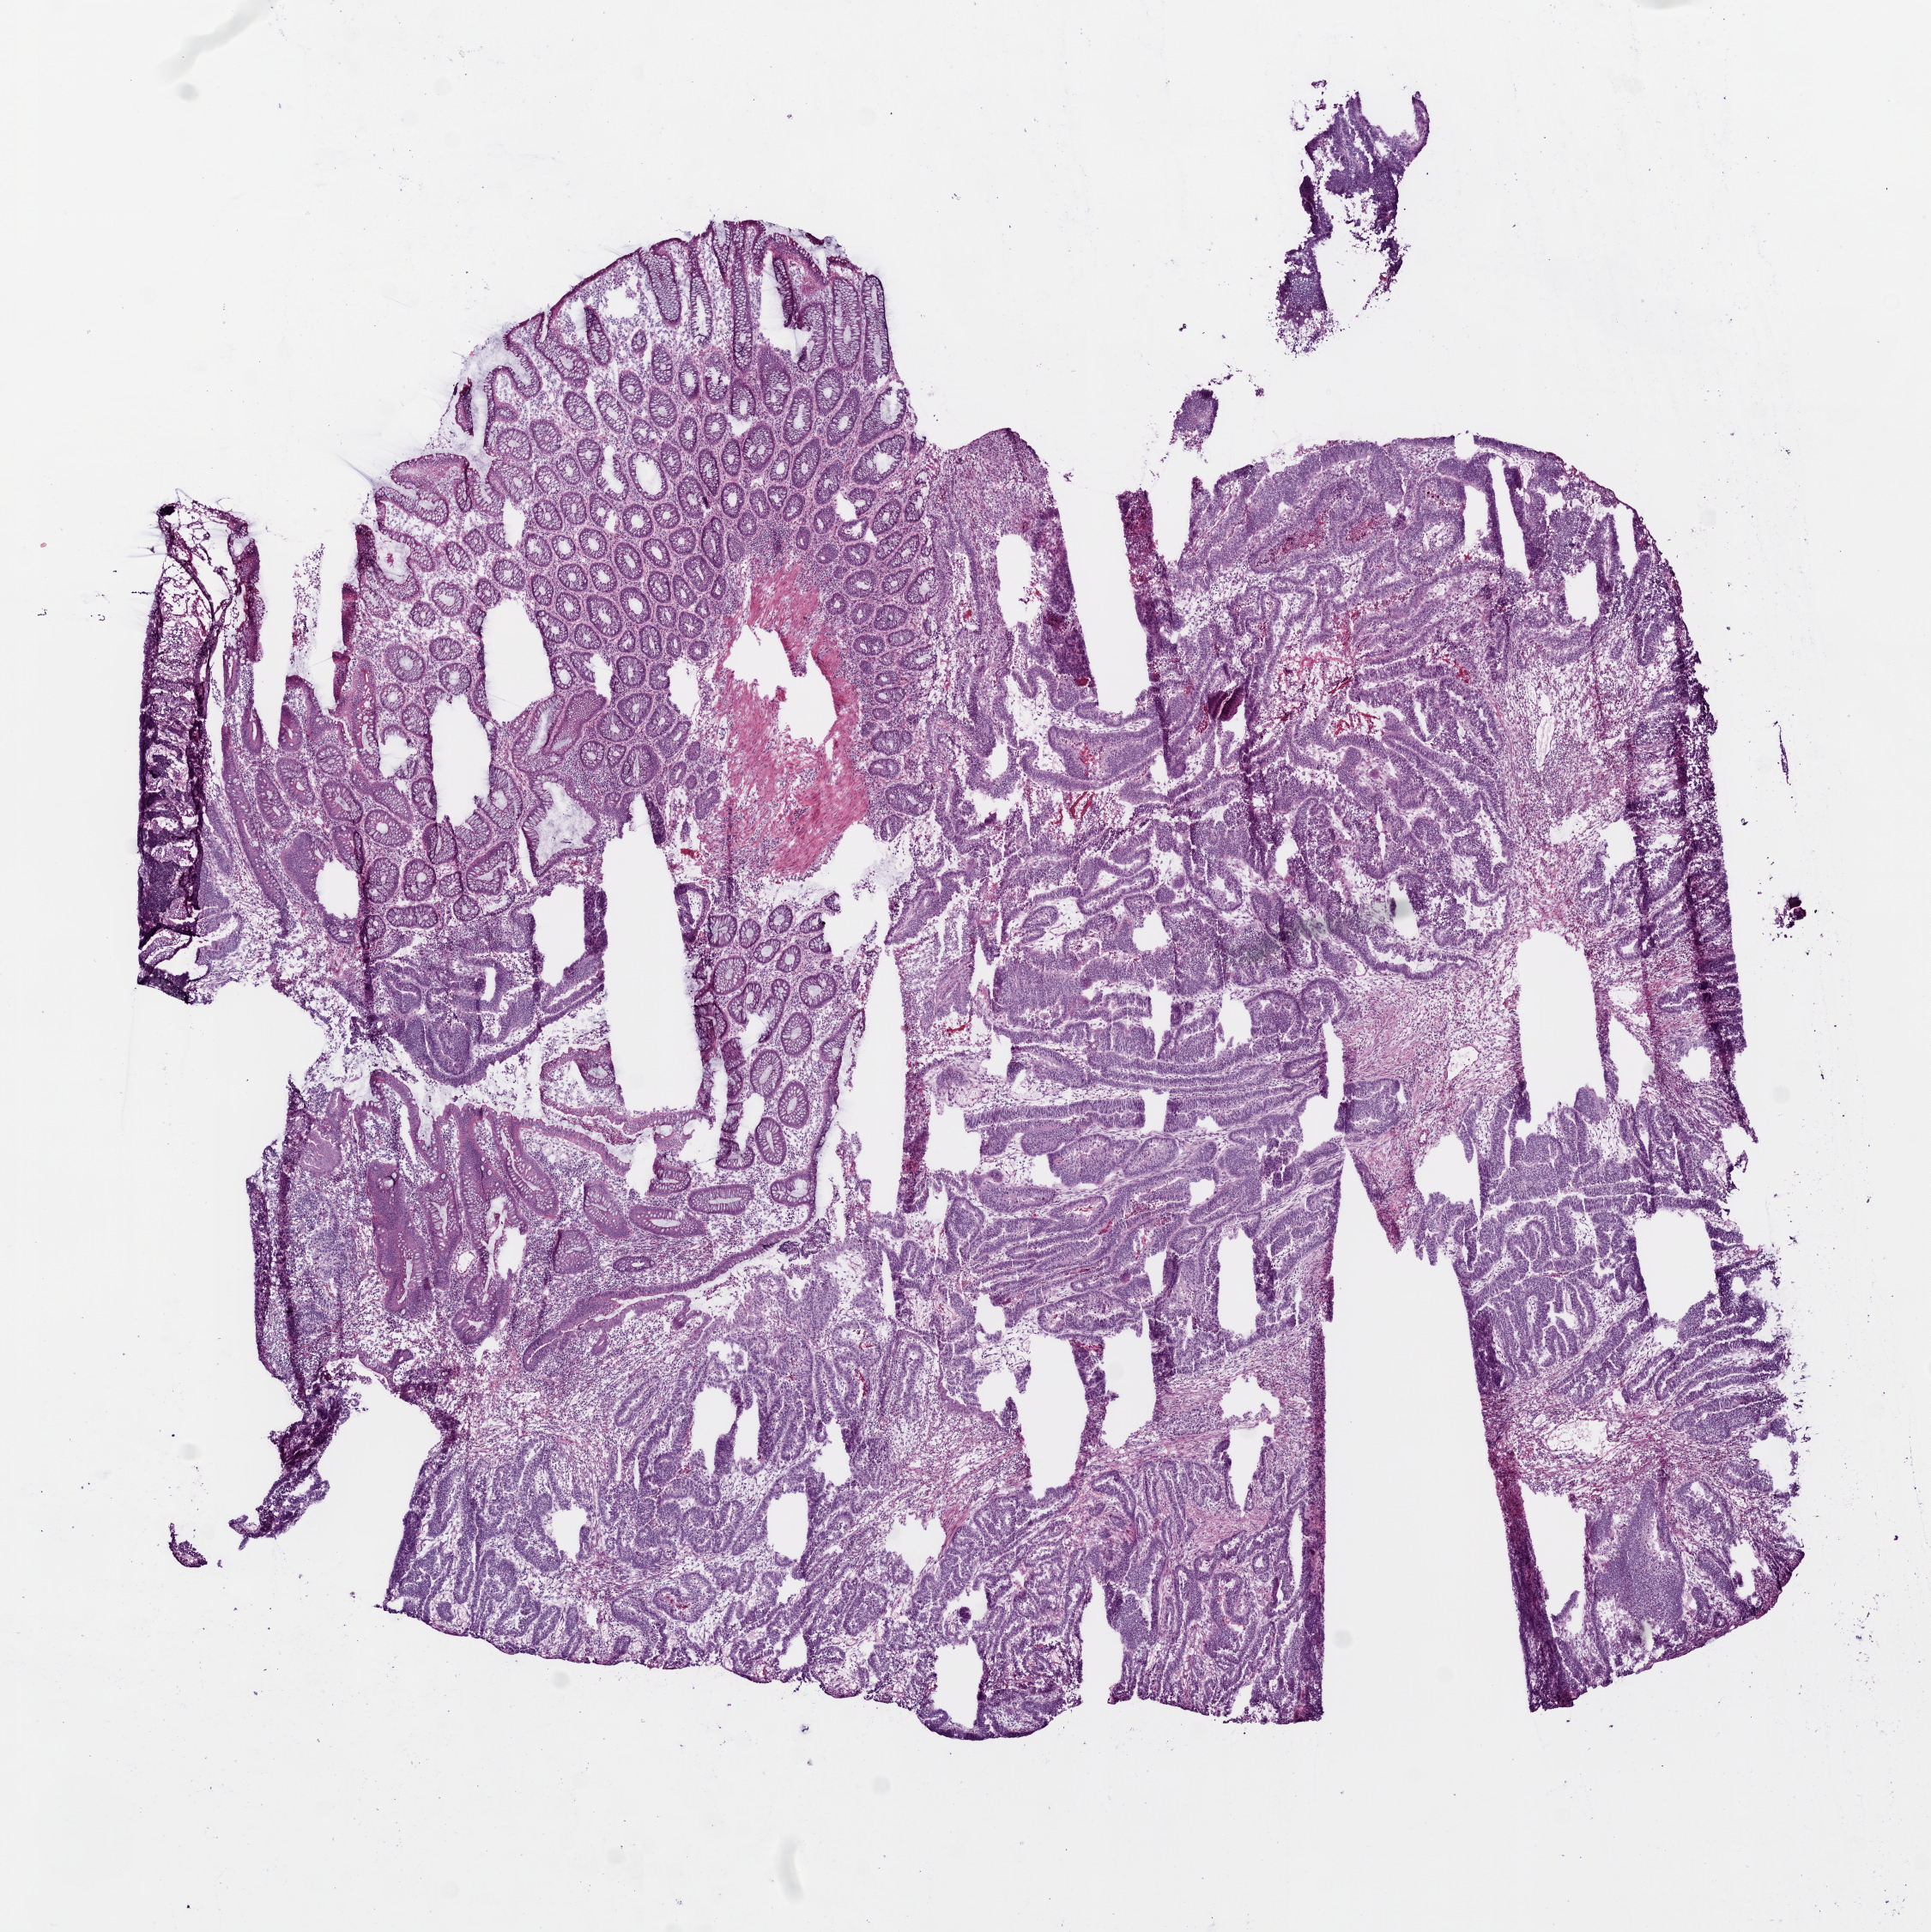
Hematoxylin and eosin (H&E) stained whole-slide image, whole scanned area (about 9.0 x 9.0 mm) shown as a low-resolution overview; frozen section from the bottom of the tissue portion; sample: primary tumour, rectum. Female, age 67 years at initial diagnosis. Composition of this section per pathologist review: tumour cells 59%, tumour nuclei 60%, normal cells 30%, stromal cells 8%, necrosis 3%.
• pathologic diagnosis: Adenocarcinoma, NOS (rectosigmoid junction)
• lymph nodes positive (case pathology): 0 of 26 examined
• AJCC pathologic stage: I (6th edition)